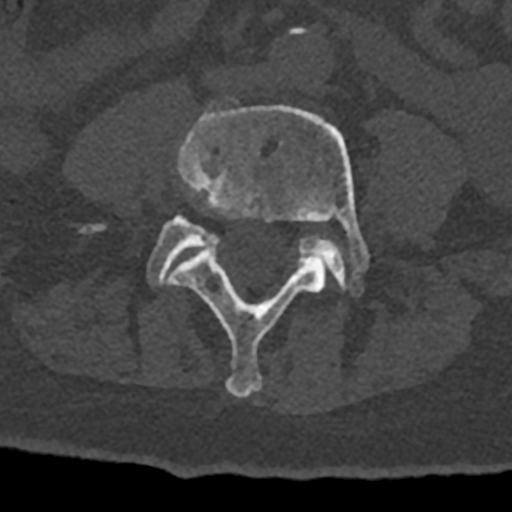
CT including the spine, one axial slice; slice 242 of 797 in the series (ordered by position); 120 kVp; bone window (W 1800 / L 400 HU); 512 × 512 image matrix. Patient: male, 74 years. Case-level facts recorded for this patient, not image findings: primary cancer: renal; vertebrae with lytic lesions (as recorded): T10, L1, L2, L3, L4, L5.
Outlined on this slice (semi-automatic segmentation, software-assisted and operator-edited):
- L4 vertebra: bounding box [x1, y1, x2, y2] px = [167, 105, 370, 397]
- L5 vertebra: [147, 216, 347, 289]